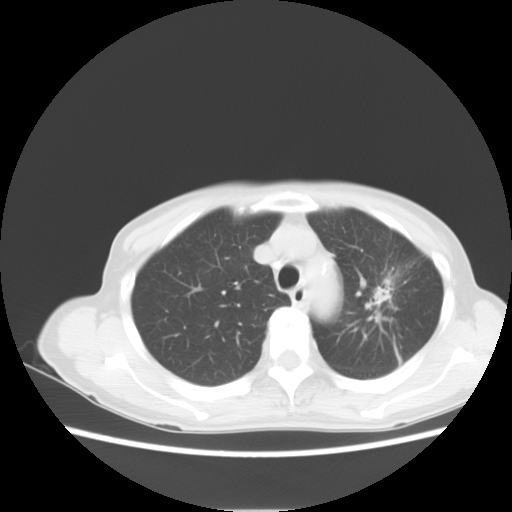
Chest CT, one axial slice. Position 7 of 11 along the scan axis. 120 kVp. Lung window (W 1500 / L -600 HU). 5 mm slice thickness. 512 × 512 image matrix, field of view 350 × 350 mm. Female patient, age 71 years. Case-level facts recorded for this patient, not image findings: clinical TNM (as recorded): T2 N0 M0.
Structures marked on this image (rectangle marked by the reading radiologist):
- lung tumour (recorded histology: adenocarcinoma): bounding box <375,284,394,309> (left, top, right, bottom; pixels)